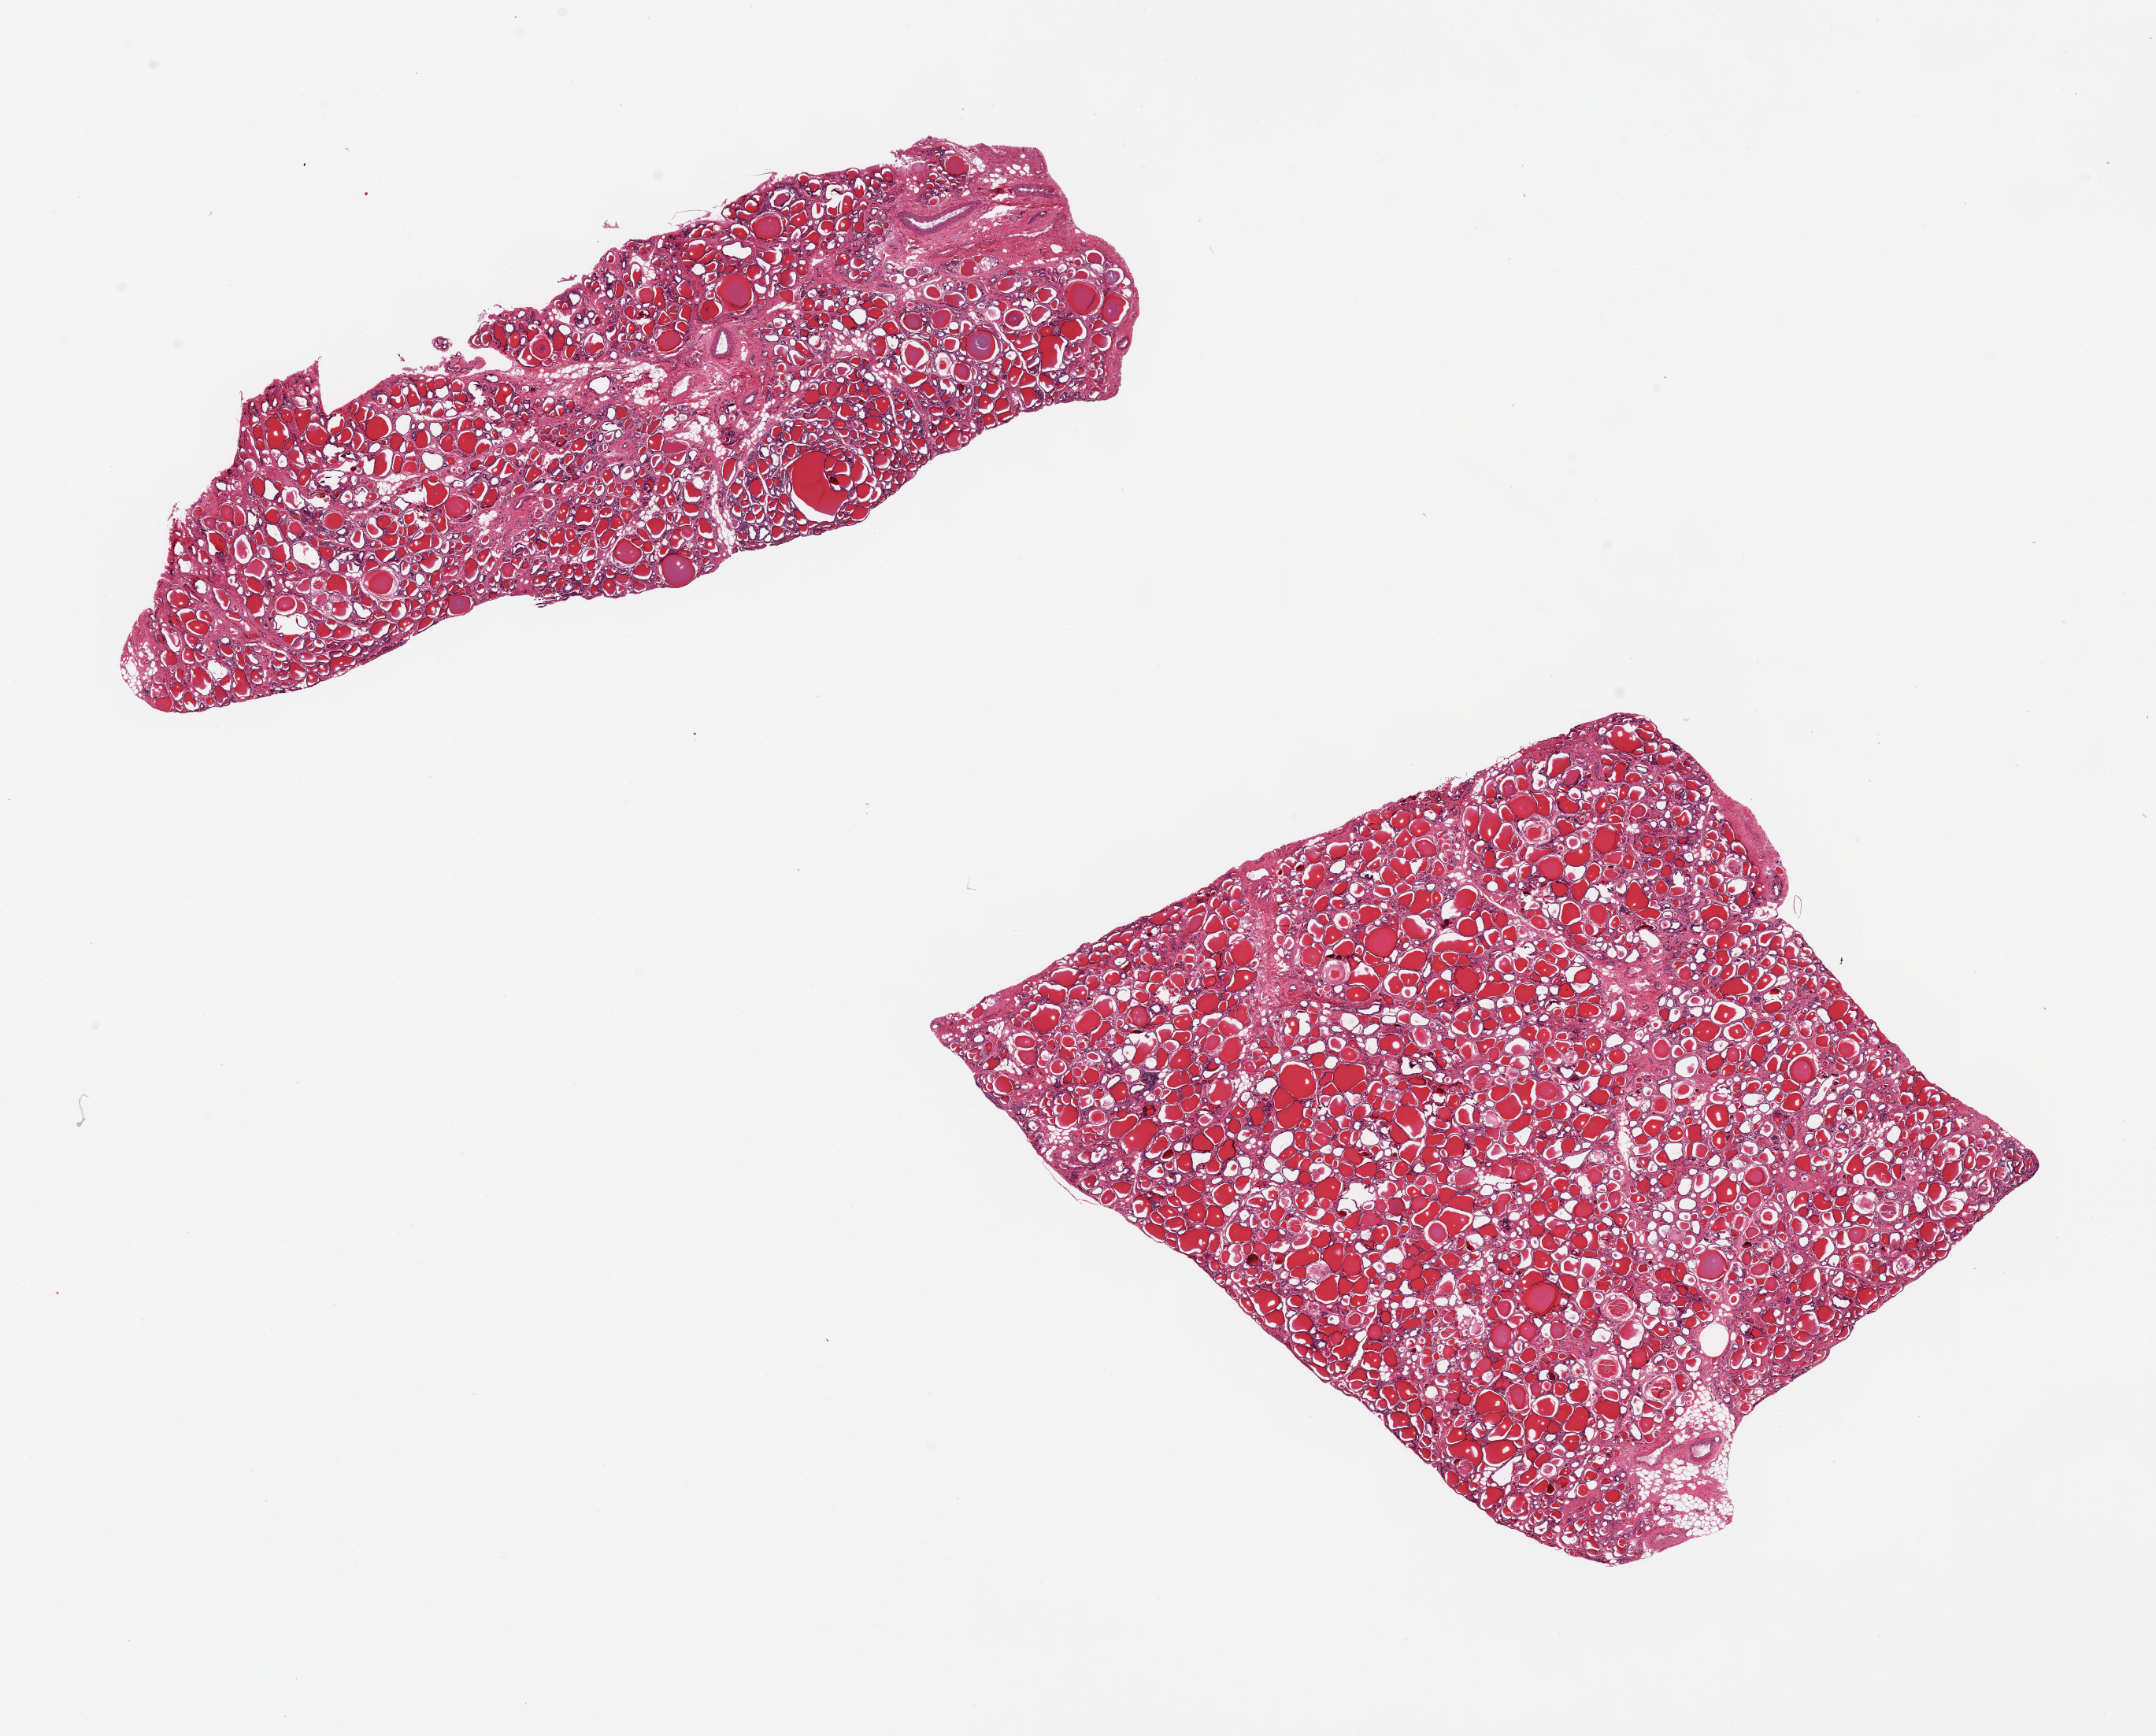
Whole-slide image, H&E stain, brightfield — shown as a low-resolution overview of the whole scanned area (about 21.7 x 17.4 mm); PAXgene-fixed paraffin-embedded (PFPE) section; section of thyroid (target tissue); donor tissue sample. Male donor.
Review note (as recorded): 2 ~10x 3-7mm pieces.